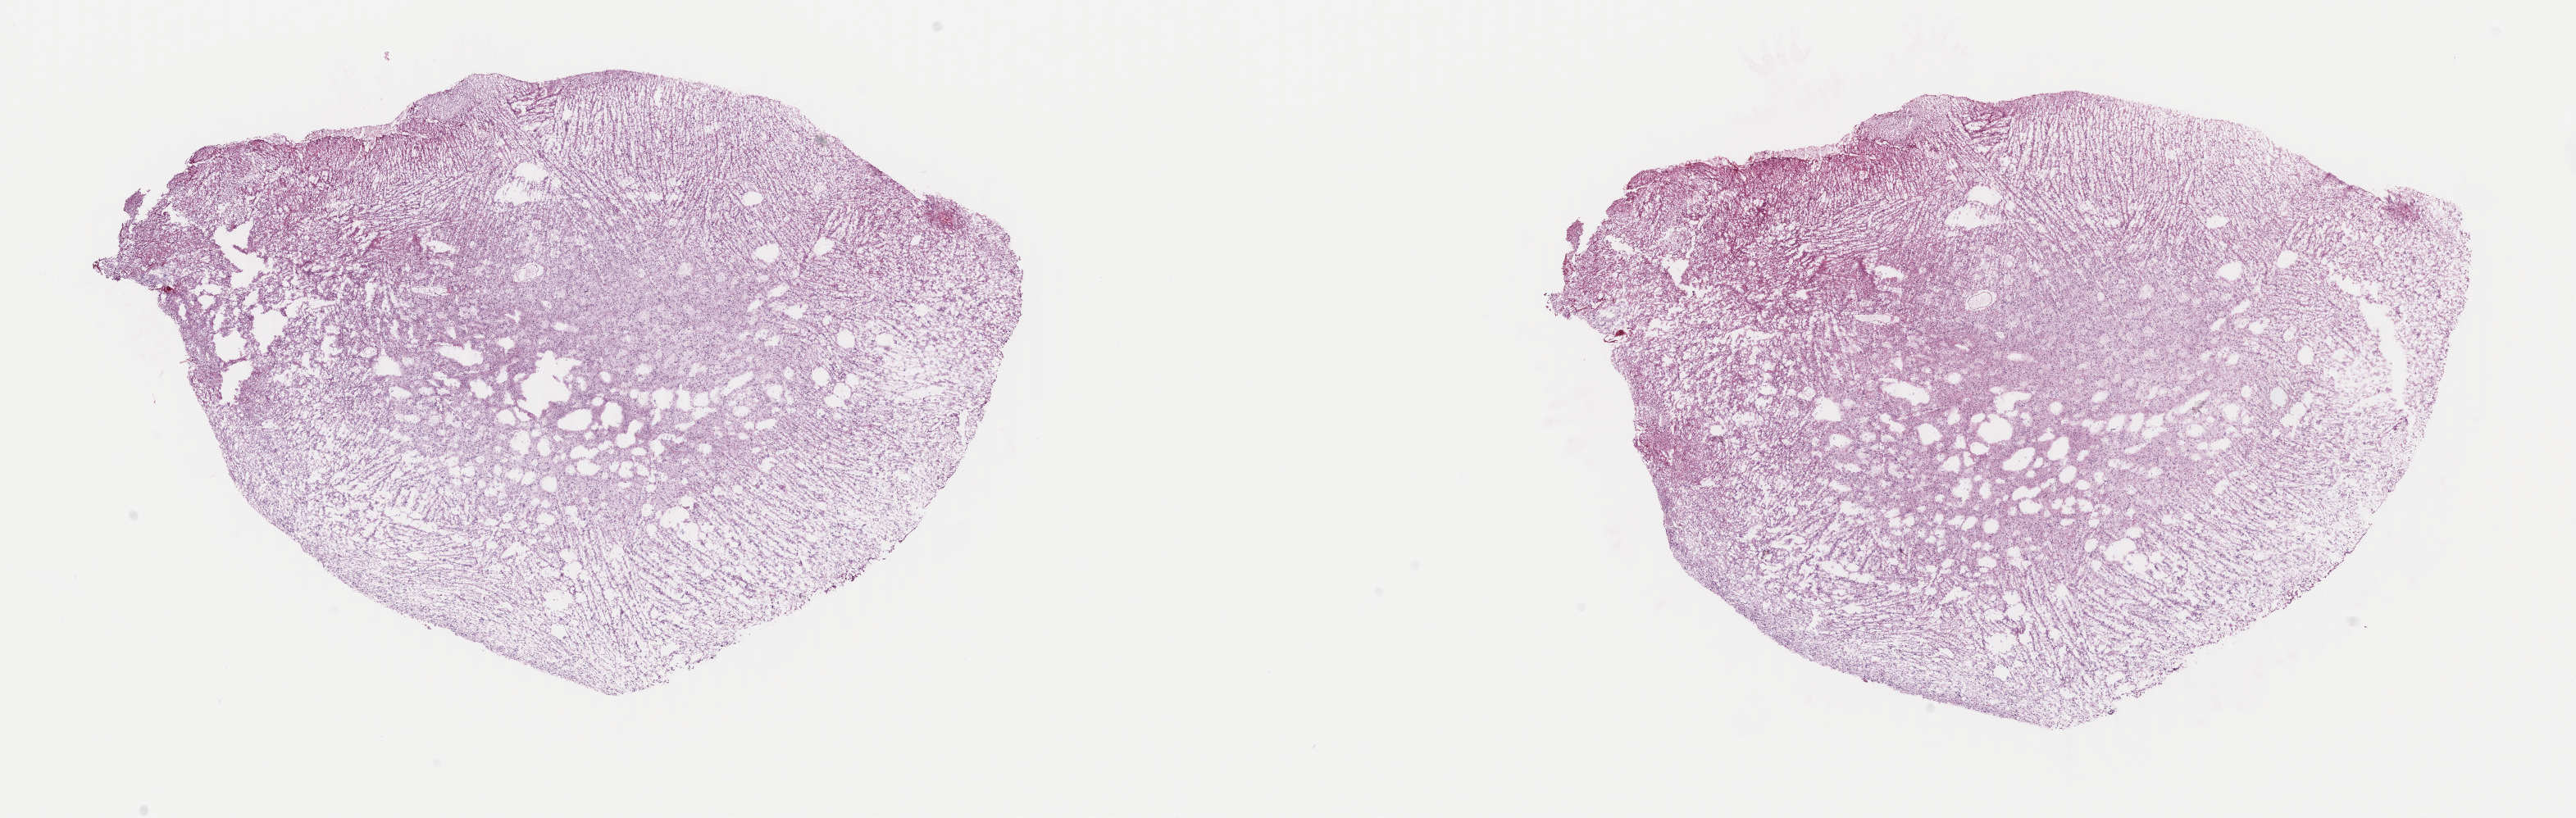
Whole-slide histology image, Hematoxylin and eosin (H&E) stained — whole scanned area (about 25.0 x 7.9 mm, acquisition: 40x scan) shown as a low-resolution overview. Frozen section. Brain, primary tumour sample. Patient: female, age at initial diagnosis 28 years. Histologic grade: G2 (moderately differentiated). Slide review estimates, as recorded: tumour cells 50%, tumour nuclei 90%, normal cells 5%, stromal cells 45%, necrosis 0%. Inflammatory infiltration, as recorded: lymphocyte infiltration 0%, monocyte infiltration 0%, neutrophil infiltration 0%.
Histologic diagnosis: Astrocytoma, NOS (cerebrum).